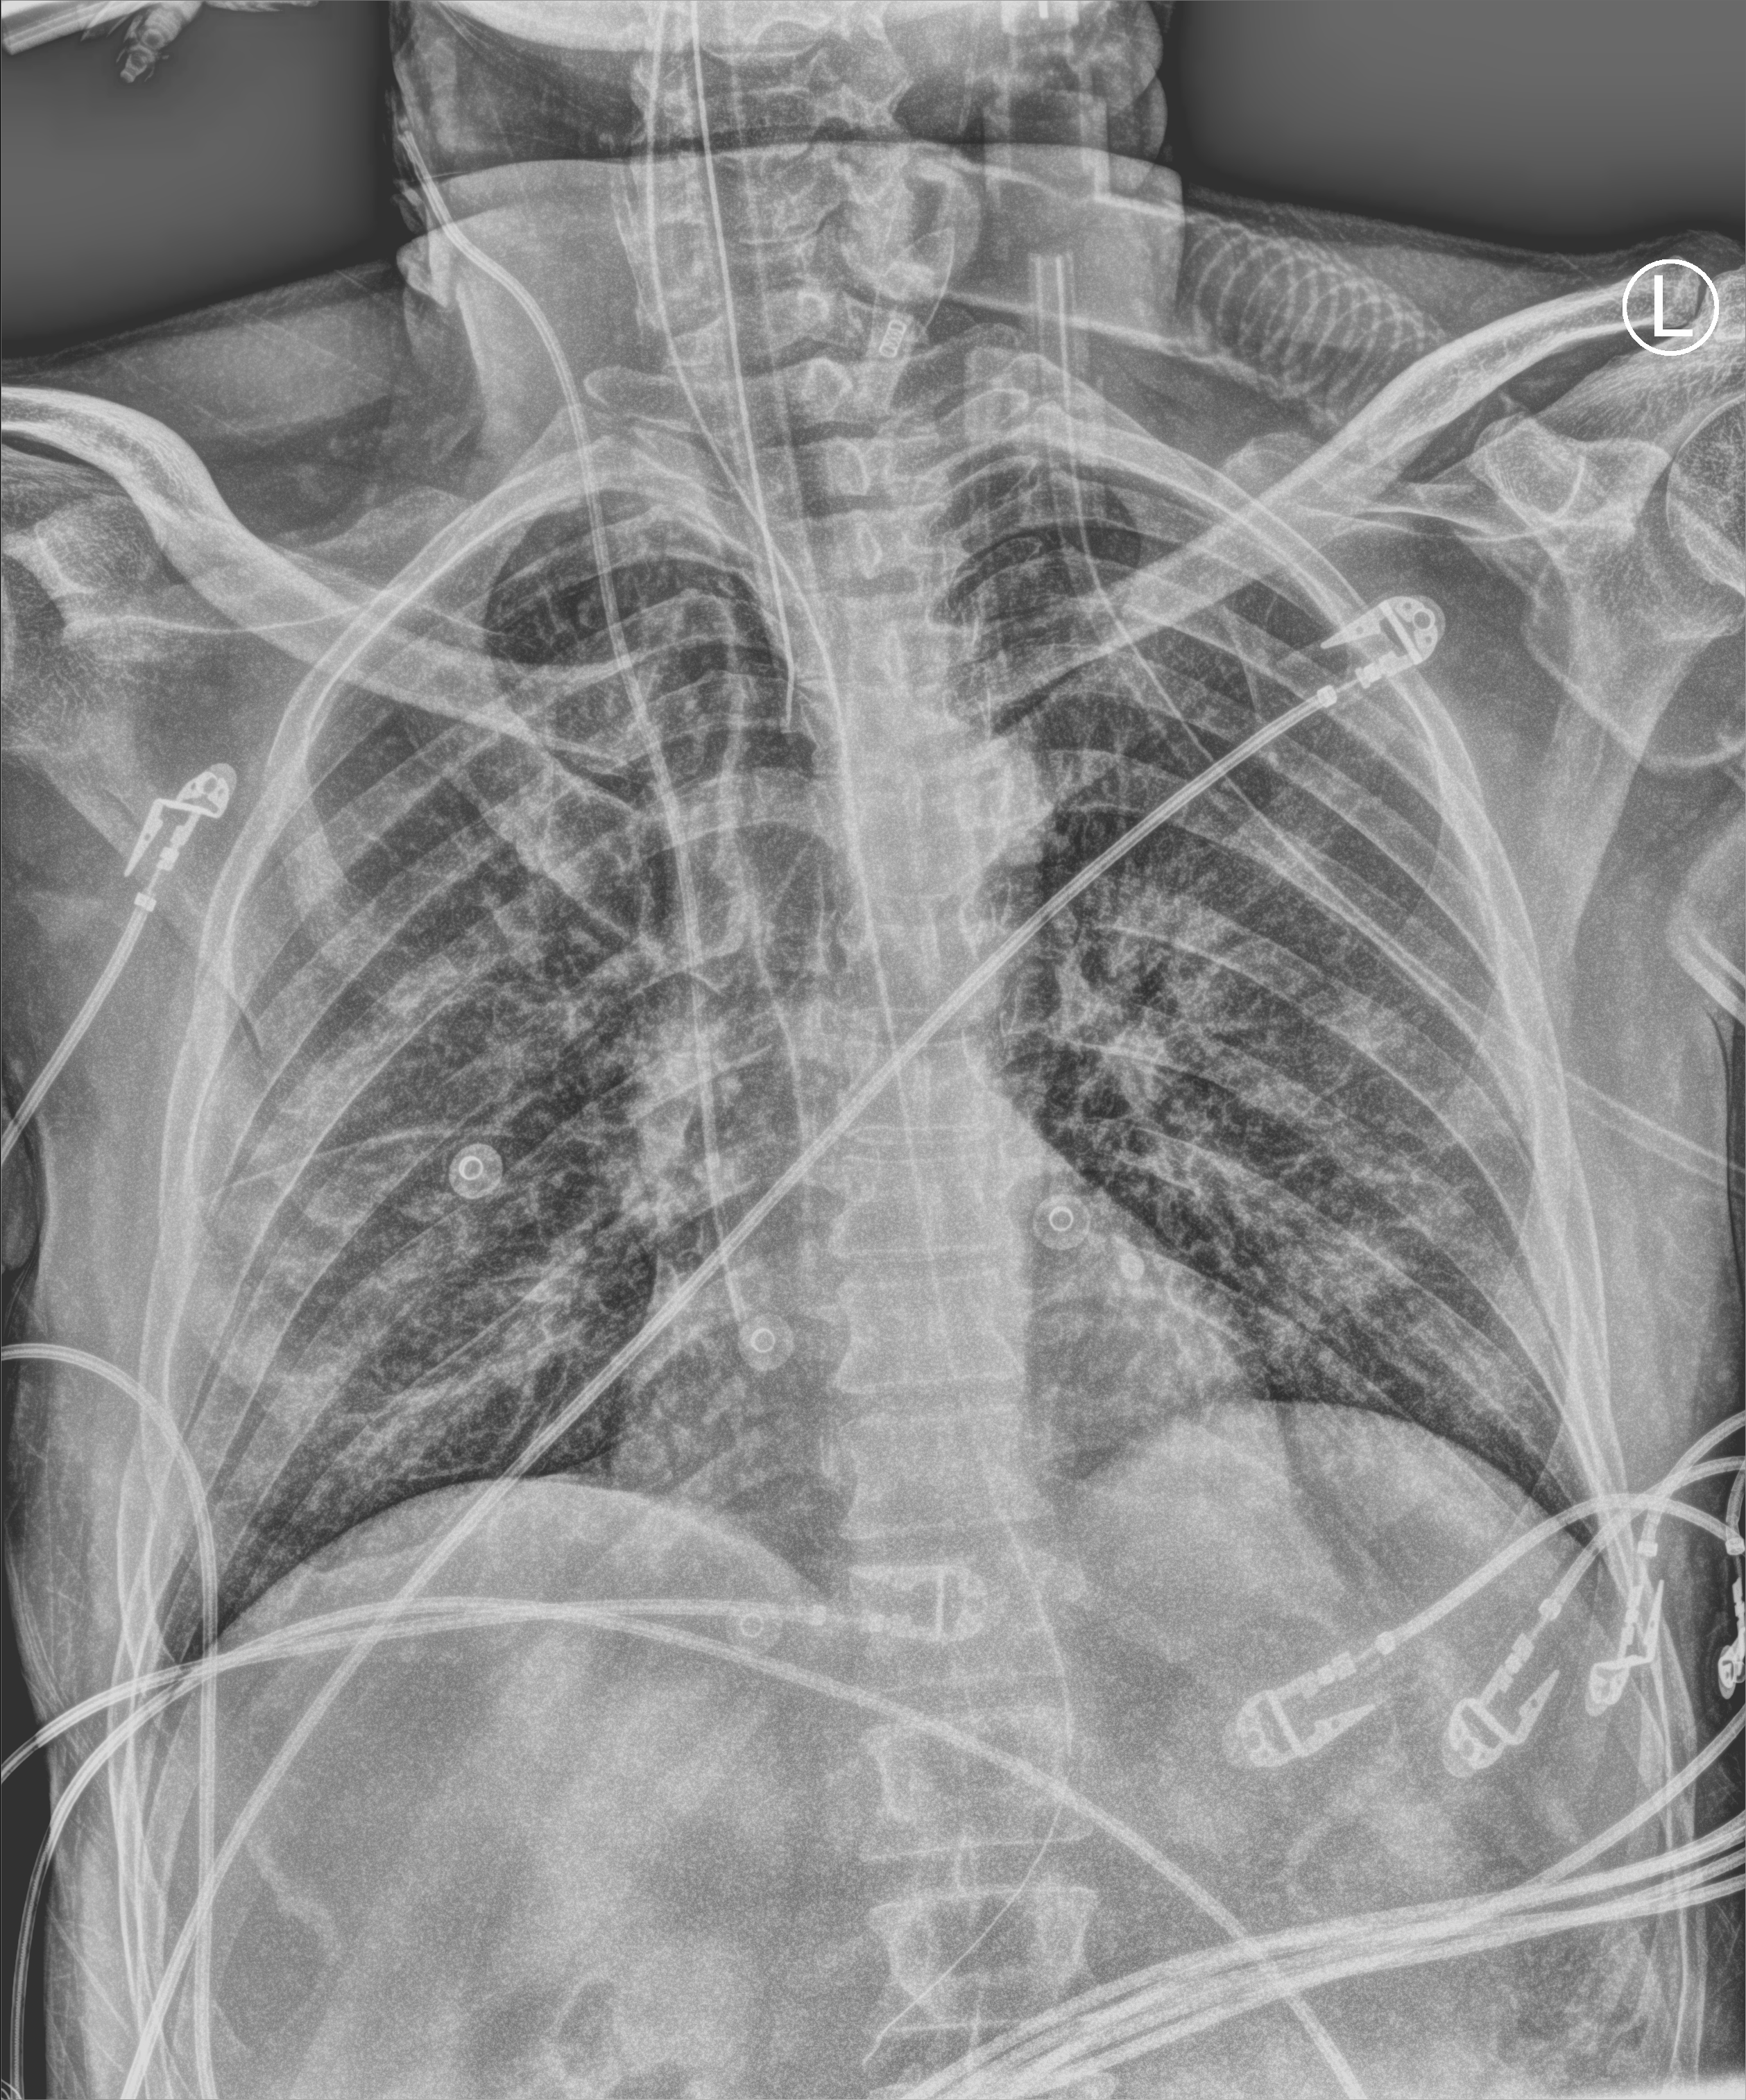
Bedside chest radiograph (computed radiography), anteroposterior (AP) projection. Male patient hospitalised with COVID-19, age 18–59 years.
Admission-level facts for this patient (not findings on this image; timing relative to this image not recorded): other chronic lung disease (admission record): no.